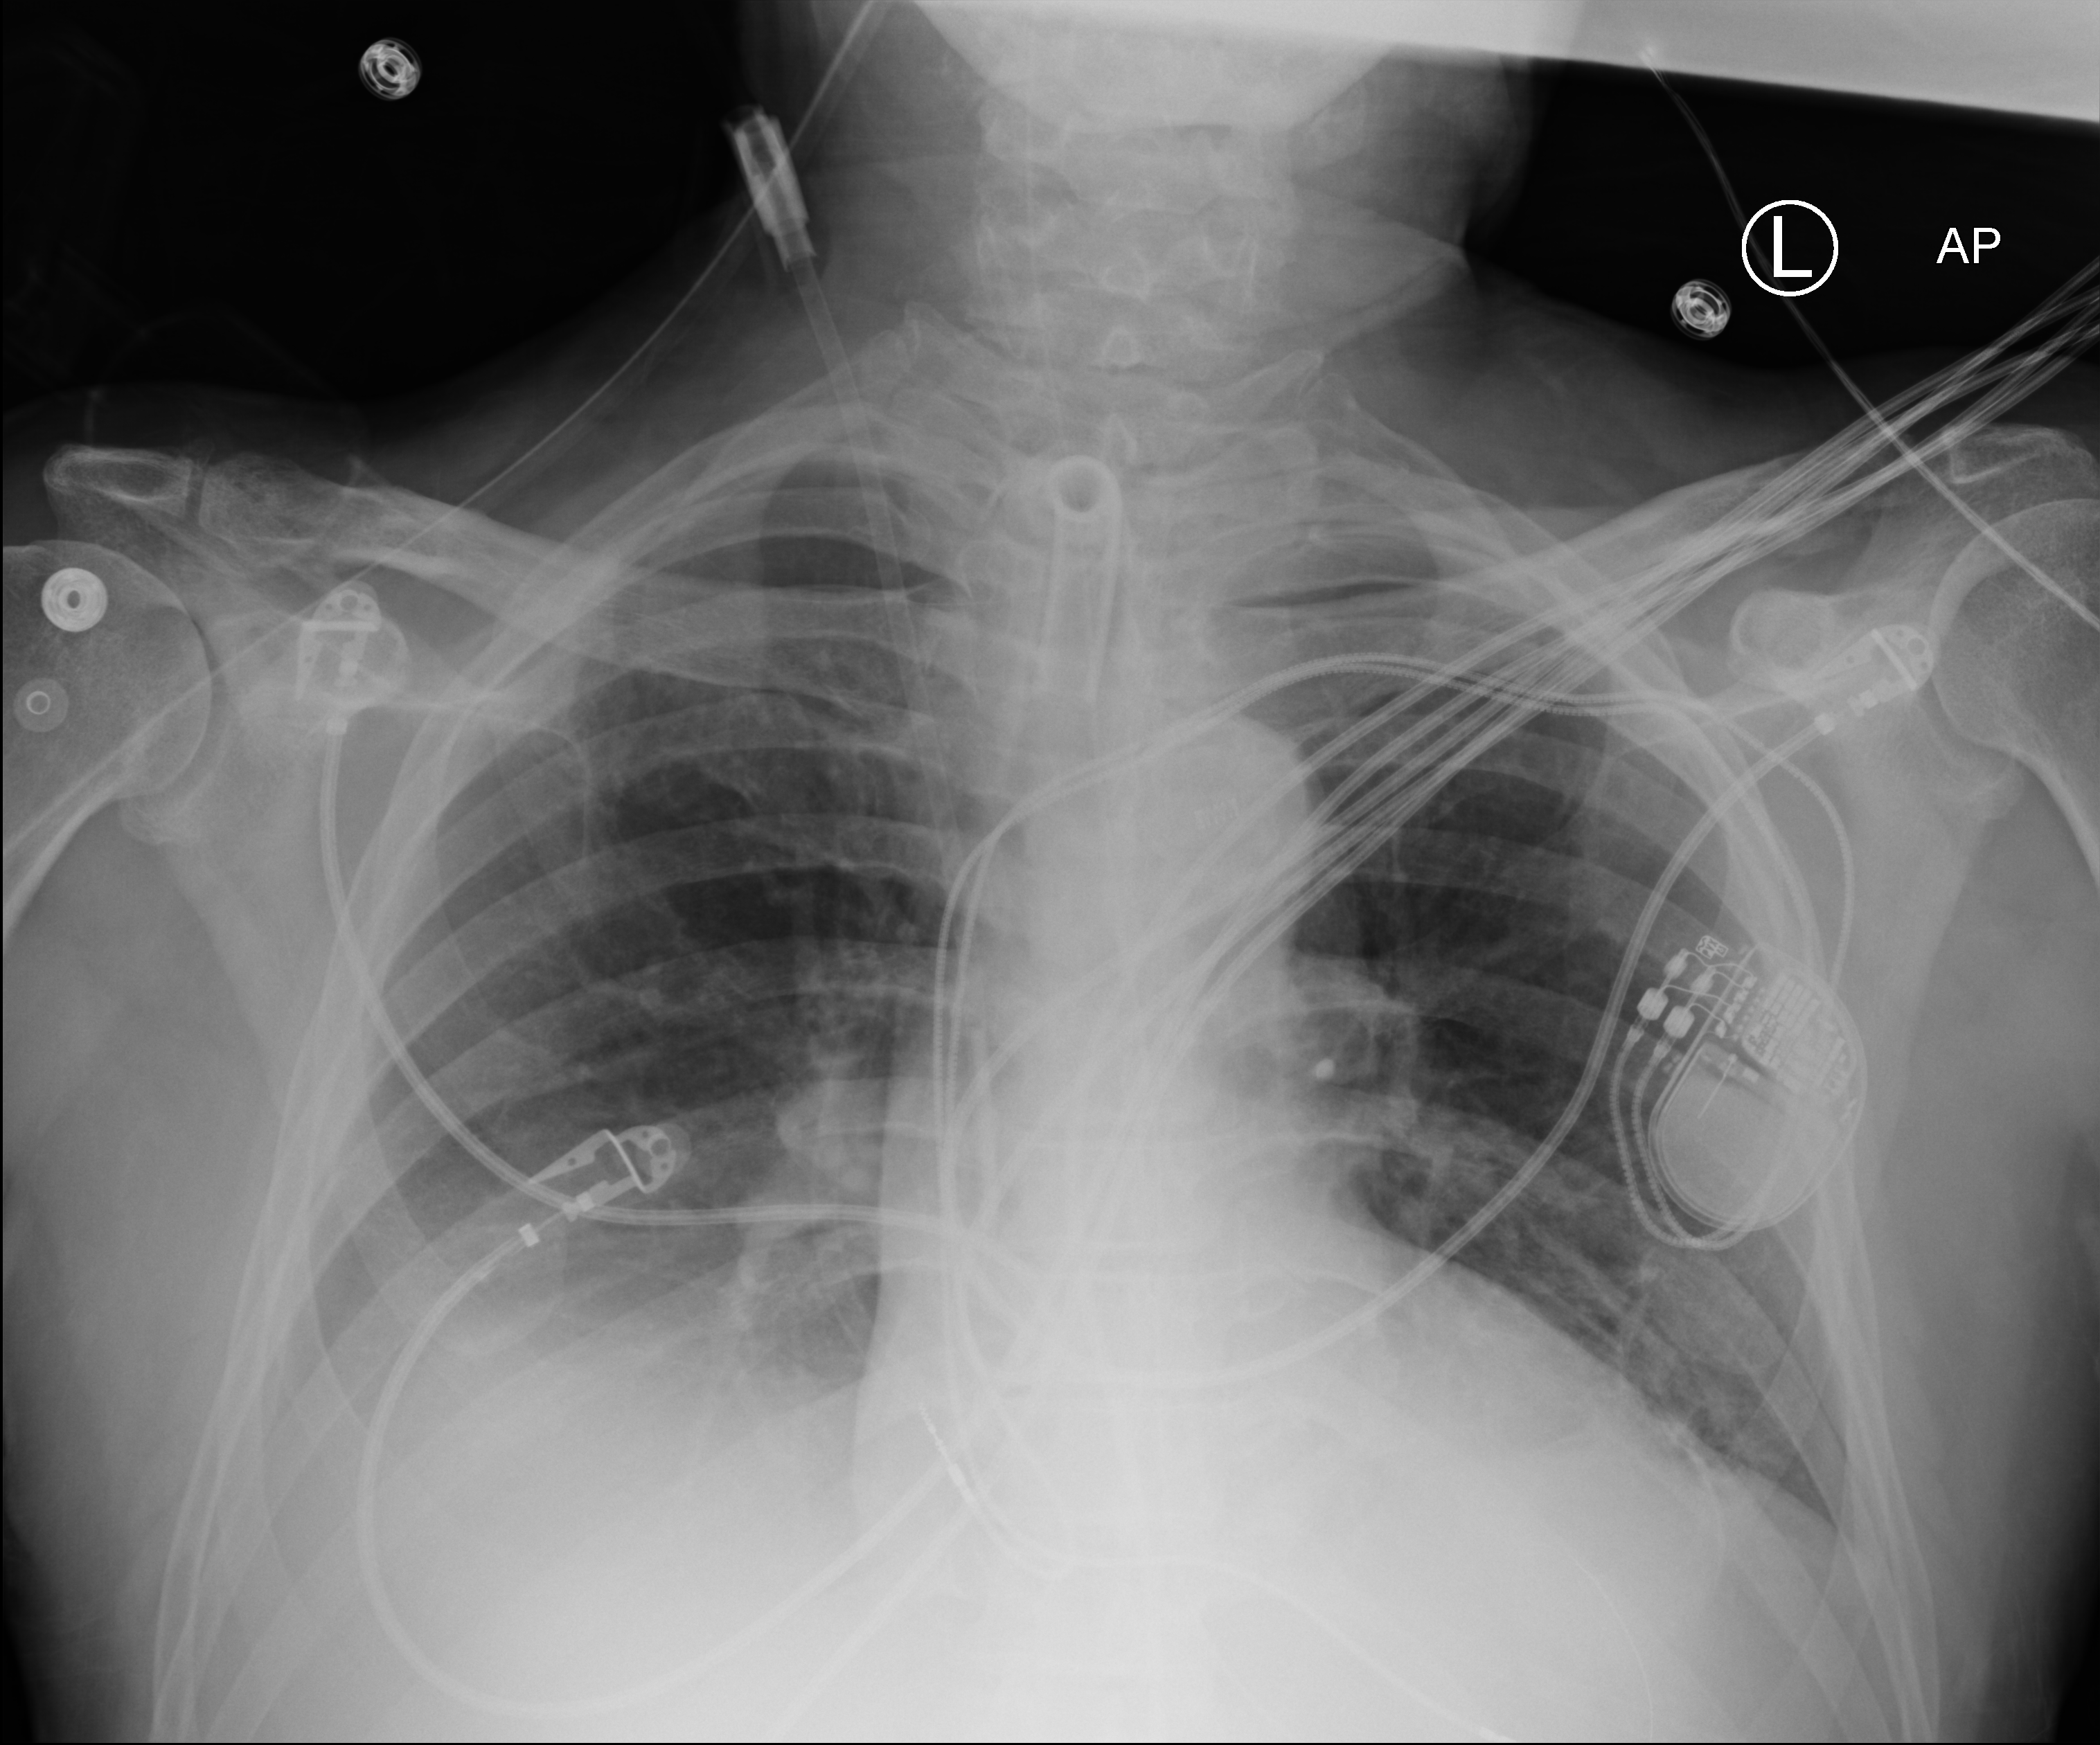
Chest X-ray (portable). Male patient hospitalised with COVID-19, age 60–74 years.
Admission-level facts for this patient (not findings on this image; timing relative to this image not recorded):
- admitted to intensive care during this hospital stay: yes
- mechanically ventilated during this hospital stay: yes